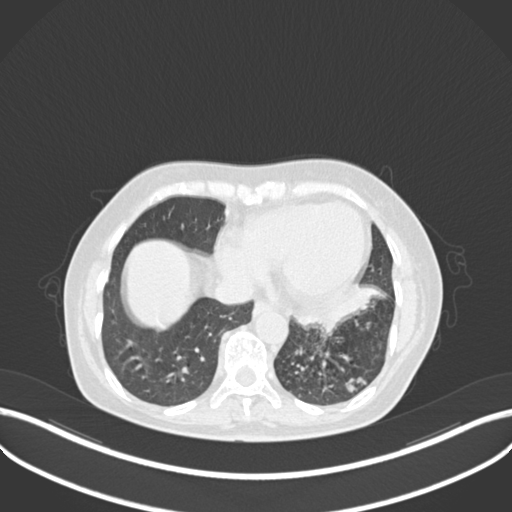
Chest CT, one axial slice. Slice 78 of 270 in the series (ordered by position). Reconstruction kernel B30f. 120 kVp. Lung window (W 1500 / L -600 HU). 1 mm slice thickness. 512 × 512 image matrix, field of view 400 × 400 mm. Patient: female, 63 years. From the clinical record (not read from this slice): clinical TNM (as recorded): T1b N0 M0; histopathological grade: G2-3.
Structures marked on this image (bounding box drawn by a radiologist):
- lung tumour (recorded histology: adenocarcinoma): box from (x=292, y=282) to (x=387, y=333) px